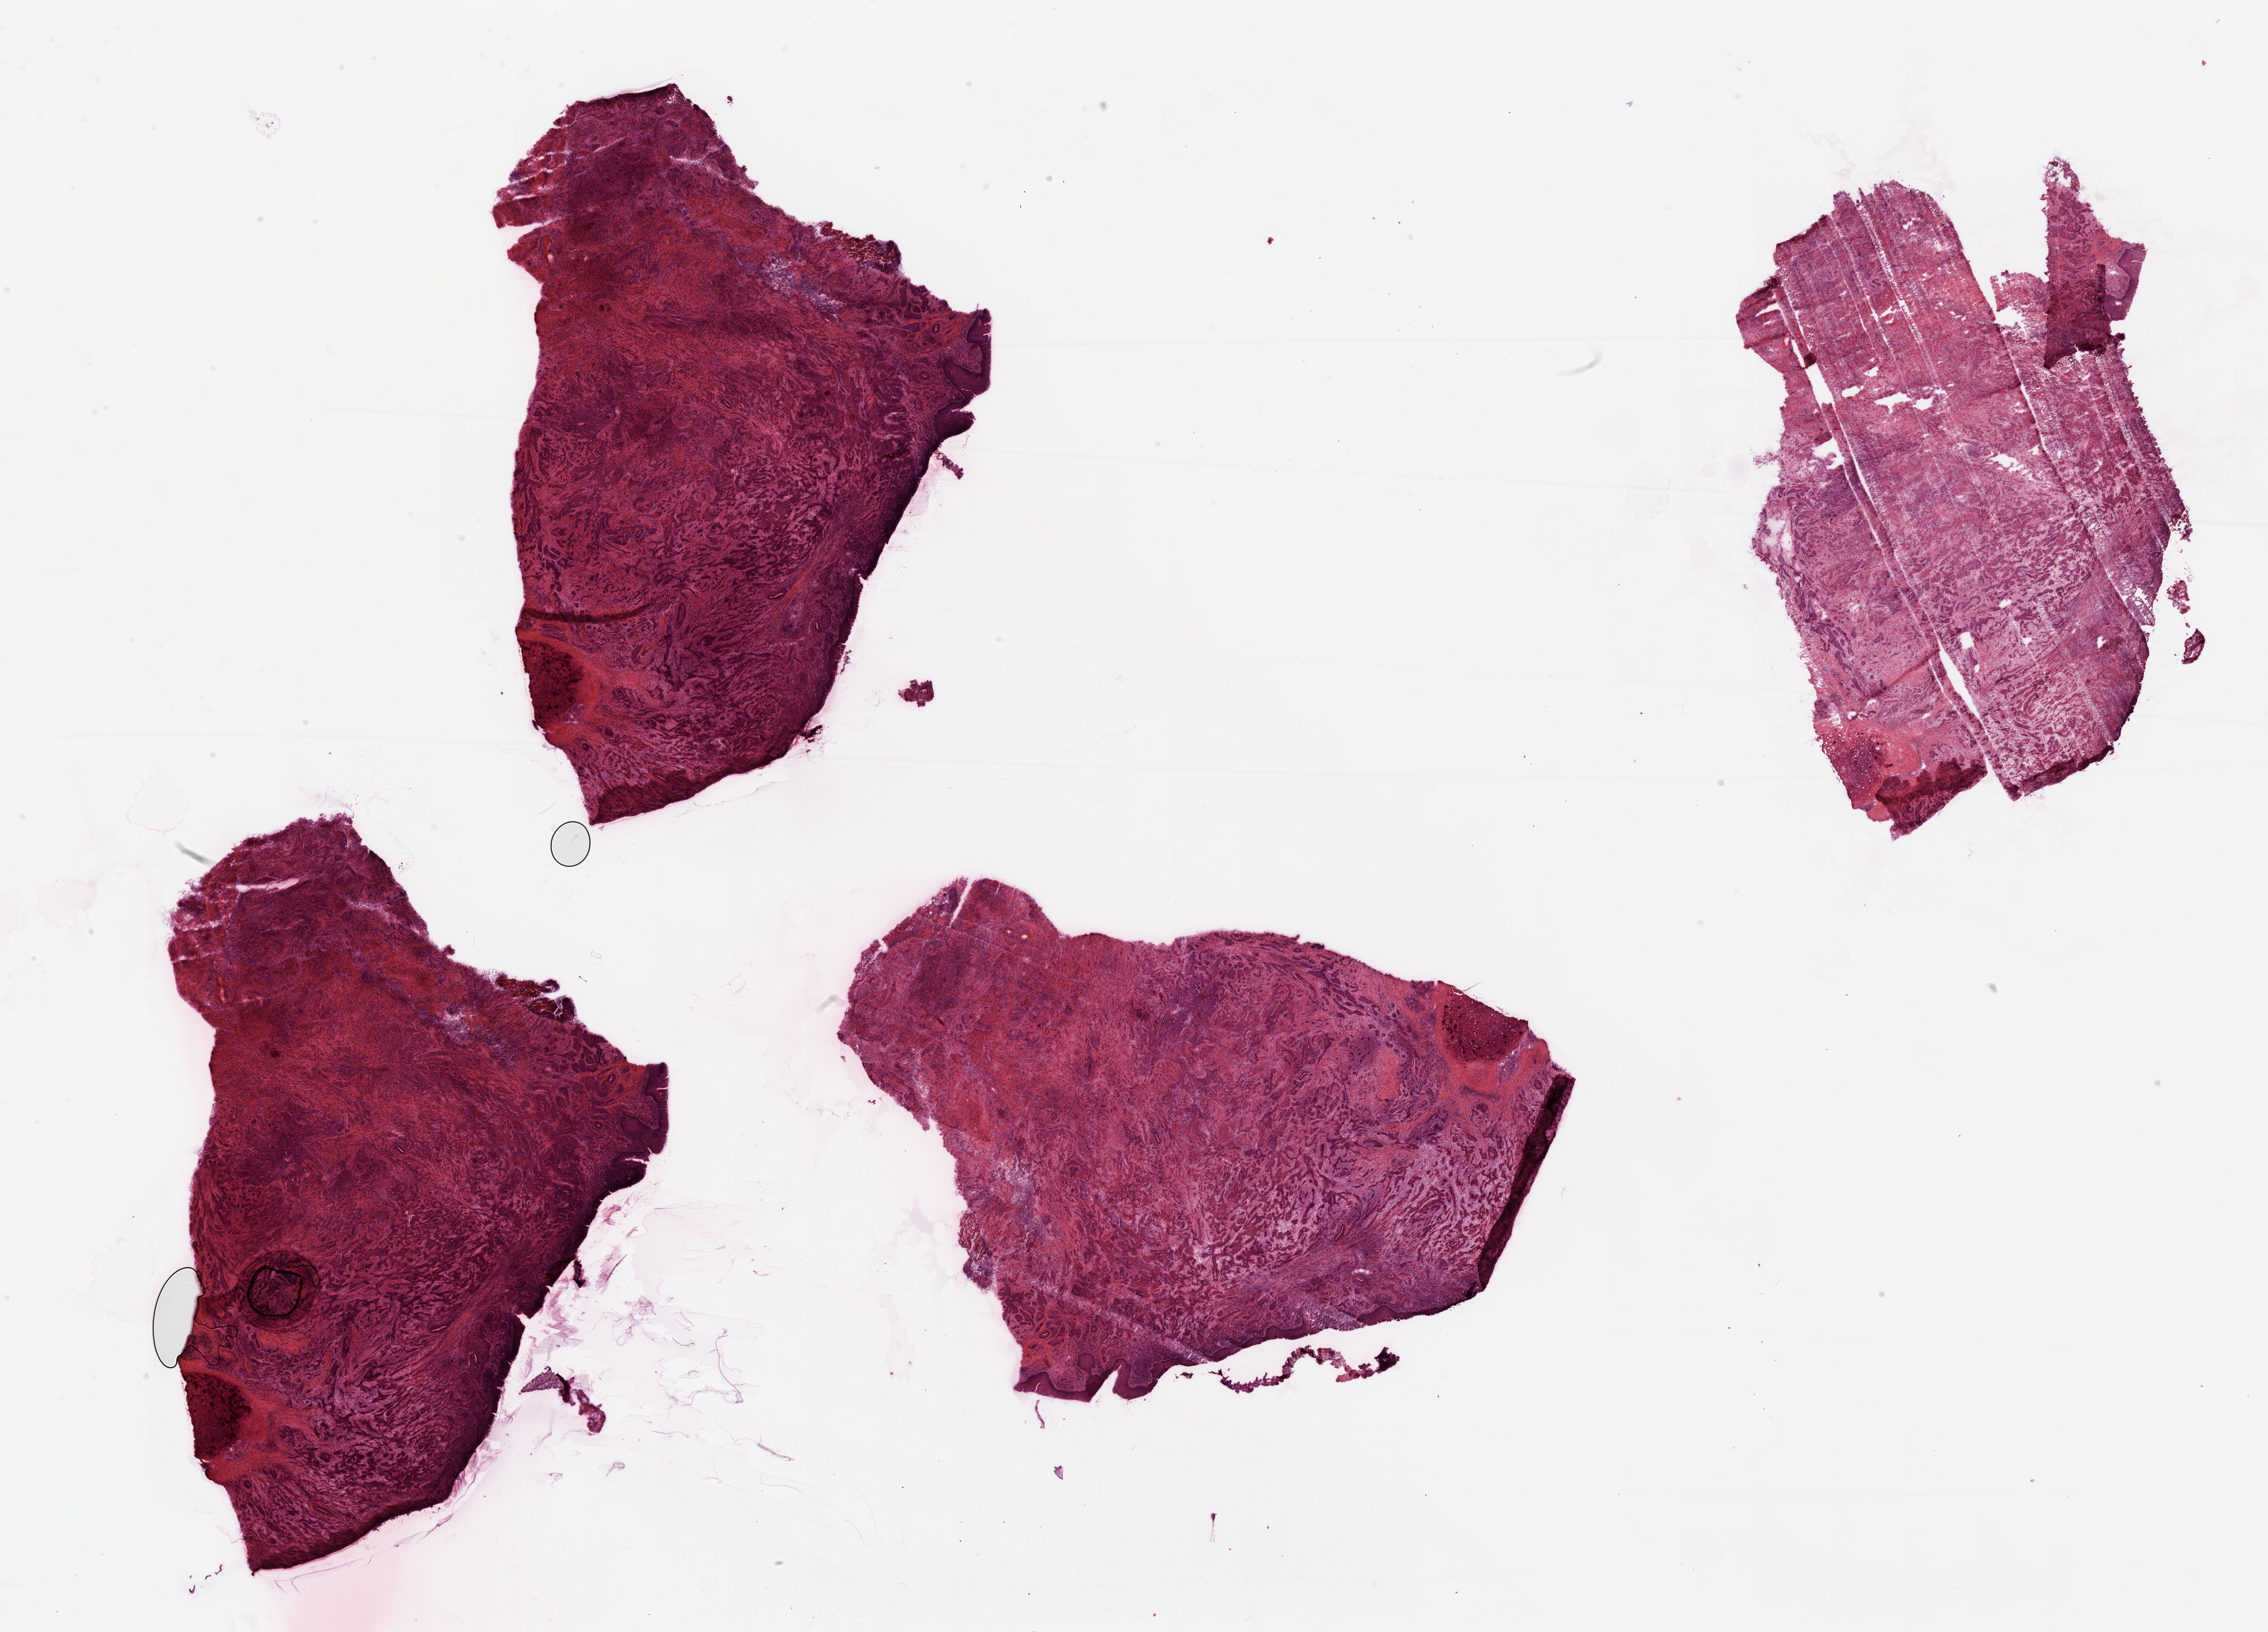
Digitized Hematoxylin and eosin (H&E) stained tissue section (whole slide), a low-resolution overview of the entire scanned area, about 30.5 x 22.0 mm (slide scanned at 20x), tumour tissue sample, sampled site: larynx. Male, 70 y/o. Histologic grade: G3 (poorly differentiated). Pathologist review of this section (percent, as recorded): tumour nuclei 80%, necrosis 5%.
Diagnosis: Squamous cell carcinoma, NOS (larynx, NOS). AJCC pathologic stage: IVA. Primary tumour site (as recorded): larynx.